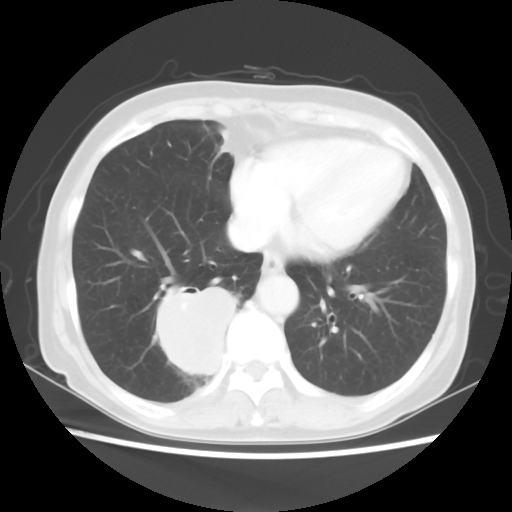
Chest CT, one axial slice. Position 18 of 56 along the scan axis. Lung window (W 1500 / L -600 HU). 5 mm slice thickness. 512 × 512 image matrix, field of view 332 × 332 mm. Patient: female, 66 years. Case-level facts recorded for this patient, not image findings: clinical TNM (as recorded): T2 N3 M0; histopathological grade: G3.
Outlined on this slice (rectangle marked by the reading radiologist):
- lung tumour (recorded histology: small cell carcinoma): bounding box <149,277,237,385> (left, top, right, bottom; pixels)